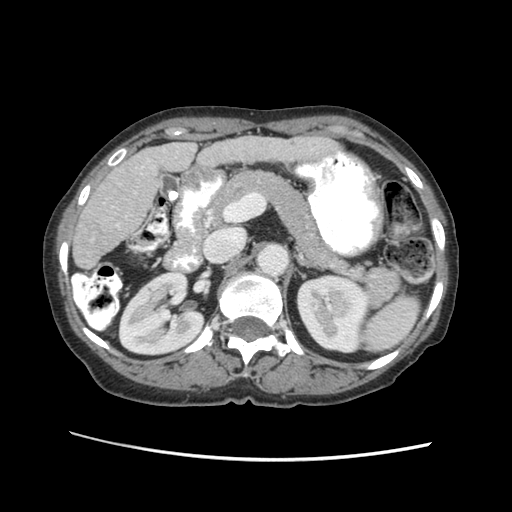
Contrast-enhanced abdominal CT (liver protocol), one axial slice. Reconstruction kernel STANDARD. Soft-tissue window (W 400 / L 40 HU). 2.5 mm slice thickness. 512 × 512 image matrix, field of view 340 × 340 mm. From the clinical record (not read from this slice): diagnosis: hepatocellular carcinoma (patient treated with transarterial chemoembolisation; whether this scan precedes or follows treatment is not stated here); TNM stage (as recorded): Stage-I; Child-Pugh class: B; tumour differentiation: well differentiated; tumour nodularity: uninodular.
Structures marked on this image (semi-automatic segmentation, software-assisted and operator-edited):
- liver parenchyma outside the tumour (the mass and vessels are separate outlines, so this box may not span the whole liver): box from (x=72, y=132) to (x=338, y=266) px
- liver vessels: (x=116, y=148)–(x=176, y=223)